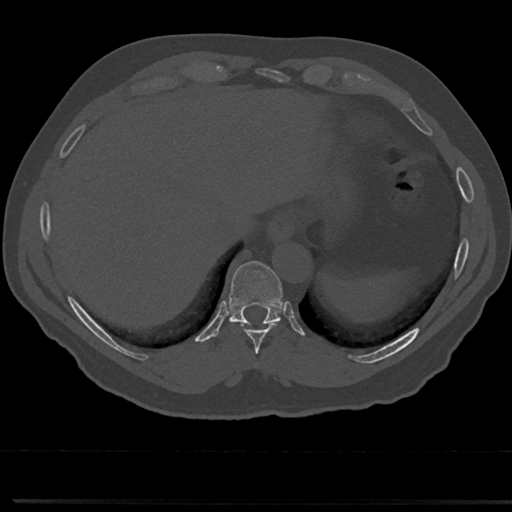
CT including the spine, one axial slice; slice 279 of 817 in the series (ordered by position); reconstruction kernel Br40s/3; 120 kVp; bone window (W 1800 / L 400 HU); 512 × 512 image matrix, field of view 355 × 355 mm. Male patient, age 61 years. From the clinical record (not read from this slice): primary cancer: prostate.
Annotated regions visible in this slice (semi-automatic segmentation, software-assisted and operator-edited):
- T10 vertebra: bounding box <231,315,279,322> (left, top, right, bottom; pixels)
- T8 vertebra: <254,322,276,371>
- T9 vertebra: <214,262,301,349>